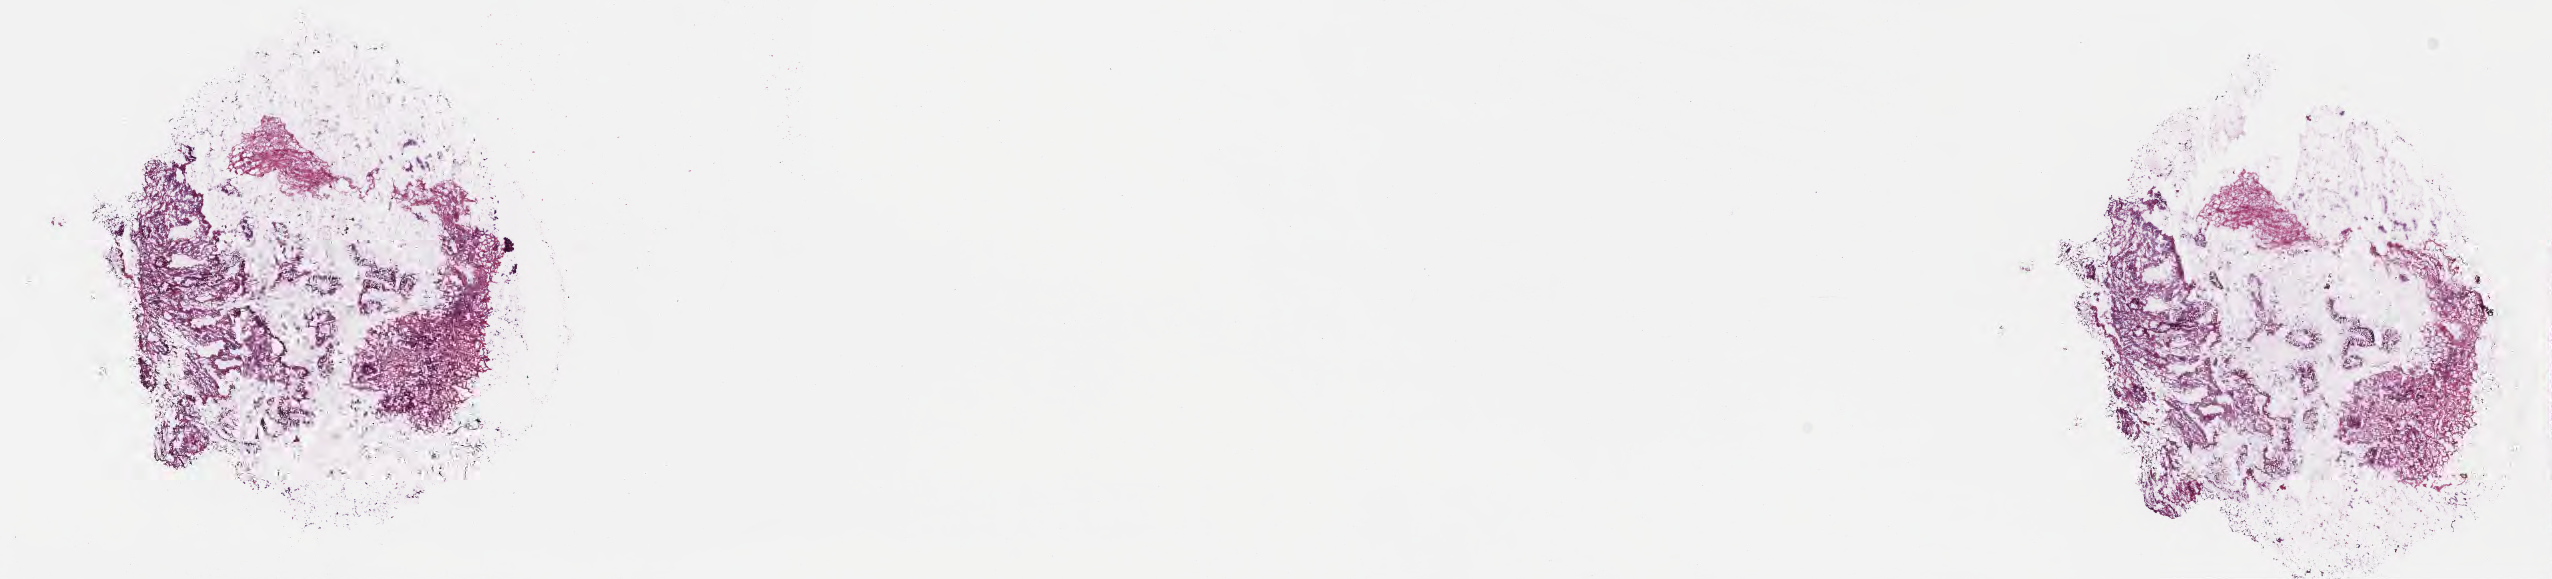
Digitized hematoxylin and eosin (H&E)-stained section, whole scanned area (about 20.6 x 4.7 mm) shown as a low-resolution overview, cryosection, primary tumor, anatomic site: rectosigmoid junction. Female, age 53 years at initial diagnosis. Tumor grade: G2 (moderately differentiated). Composition of this section per pathologist review: tumor cells 35%, tumor nuclei 35%, stromal cells 38%, necrosis 2%, normal cells 25%. Inflammatory infiltration, as recorded: lymphocyte infiltration 8%, monocyte infiltration 6%, neutrophil infiltration 10%.
AJCC pathologic stage: Stage IIIB. Histologic diagnosis: Adenocarcinoma, NOS. Section: bottom of the tissue portion.